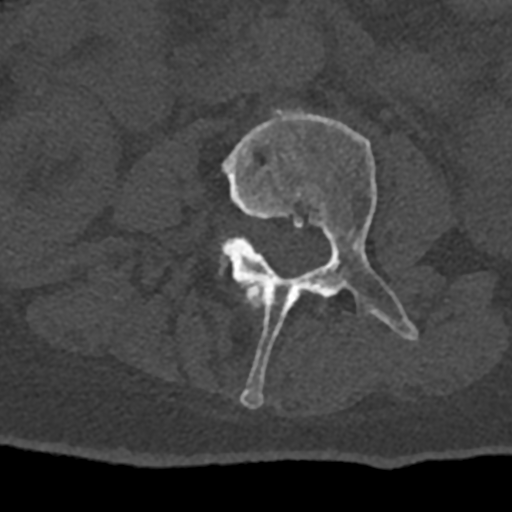
CT including the spine, one axial slice. Slice 316 of 797 in the series (ordered by position). Reconstruction kernel Br40s/3. 120 kVp. Bone window (W 1800 / L 400 HU). 512 × 512 image matrix. Male patient, age 74 years. From the clinical record (not read from this slice): primary cancer: renal.
Outlined on this slice (semi-automatic segmentation, software-assisted and operator-edited):
- L2 vertebra: bounding box (x1, y1, x2, y2) in pixels: (246, 286, 262, 309)
- L3 vertebra: (220, 109, 418, 408)
- L4 vertebra: (222, 251, 225, 256)